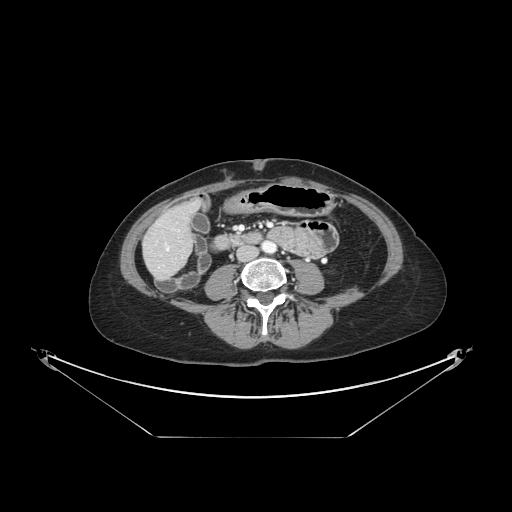
Contrast-enhanced abdominal CT, one axial slice; slice 32 of 148 in the series (ordered by position); reconstruction kernel STANDARD; intravenous contrast given; soft-tissue window (W 400 / L 40 HU); 512 × 512 image matrix. Female patient, age 73 years. From the clinical record (not read from this slice): diagnosis: colorectal cancer liver metastases, imaged before liver resection; multiple liver metastases: no; largest metastasis: 1 cm; chemotherapy before resection: yes.
Structures marked on this image (outlined manually by an expert reader):
- hepatic veins: bounding box (x1, y1, x2, y2) in pixels: (167, 247, 169, 250)
- liver: (145, 204, 196, 278)
- planned liver remnant (the part of the liver to remain after resection): (162, 204, 195, 237)